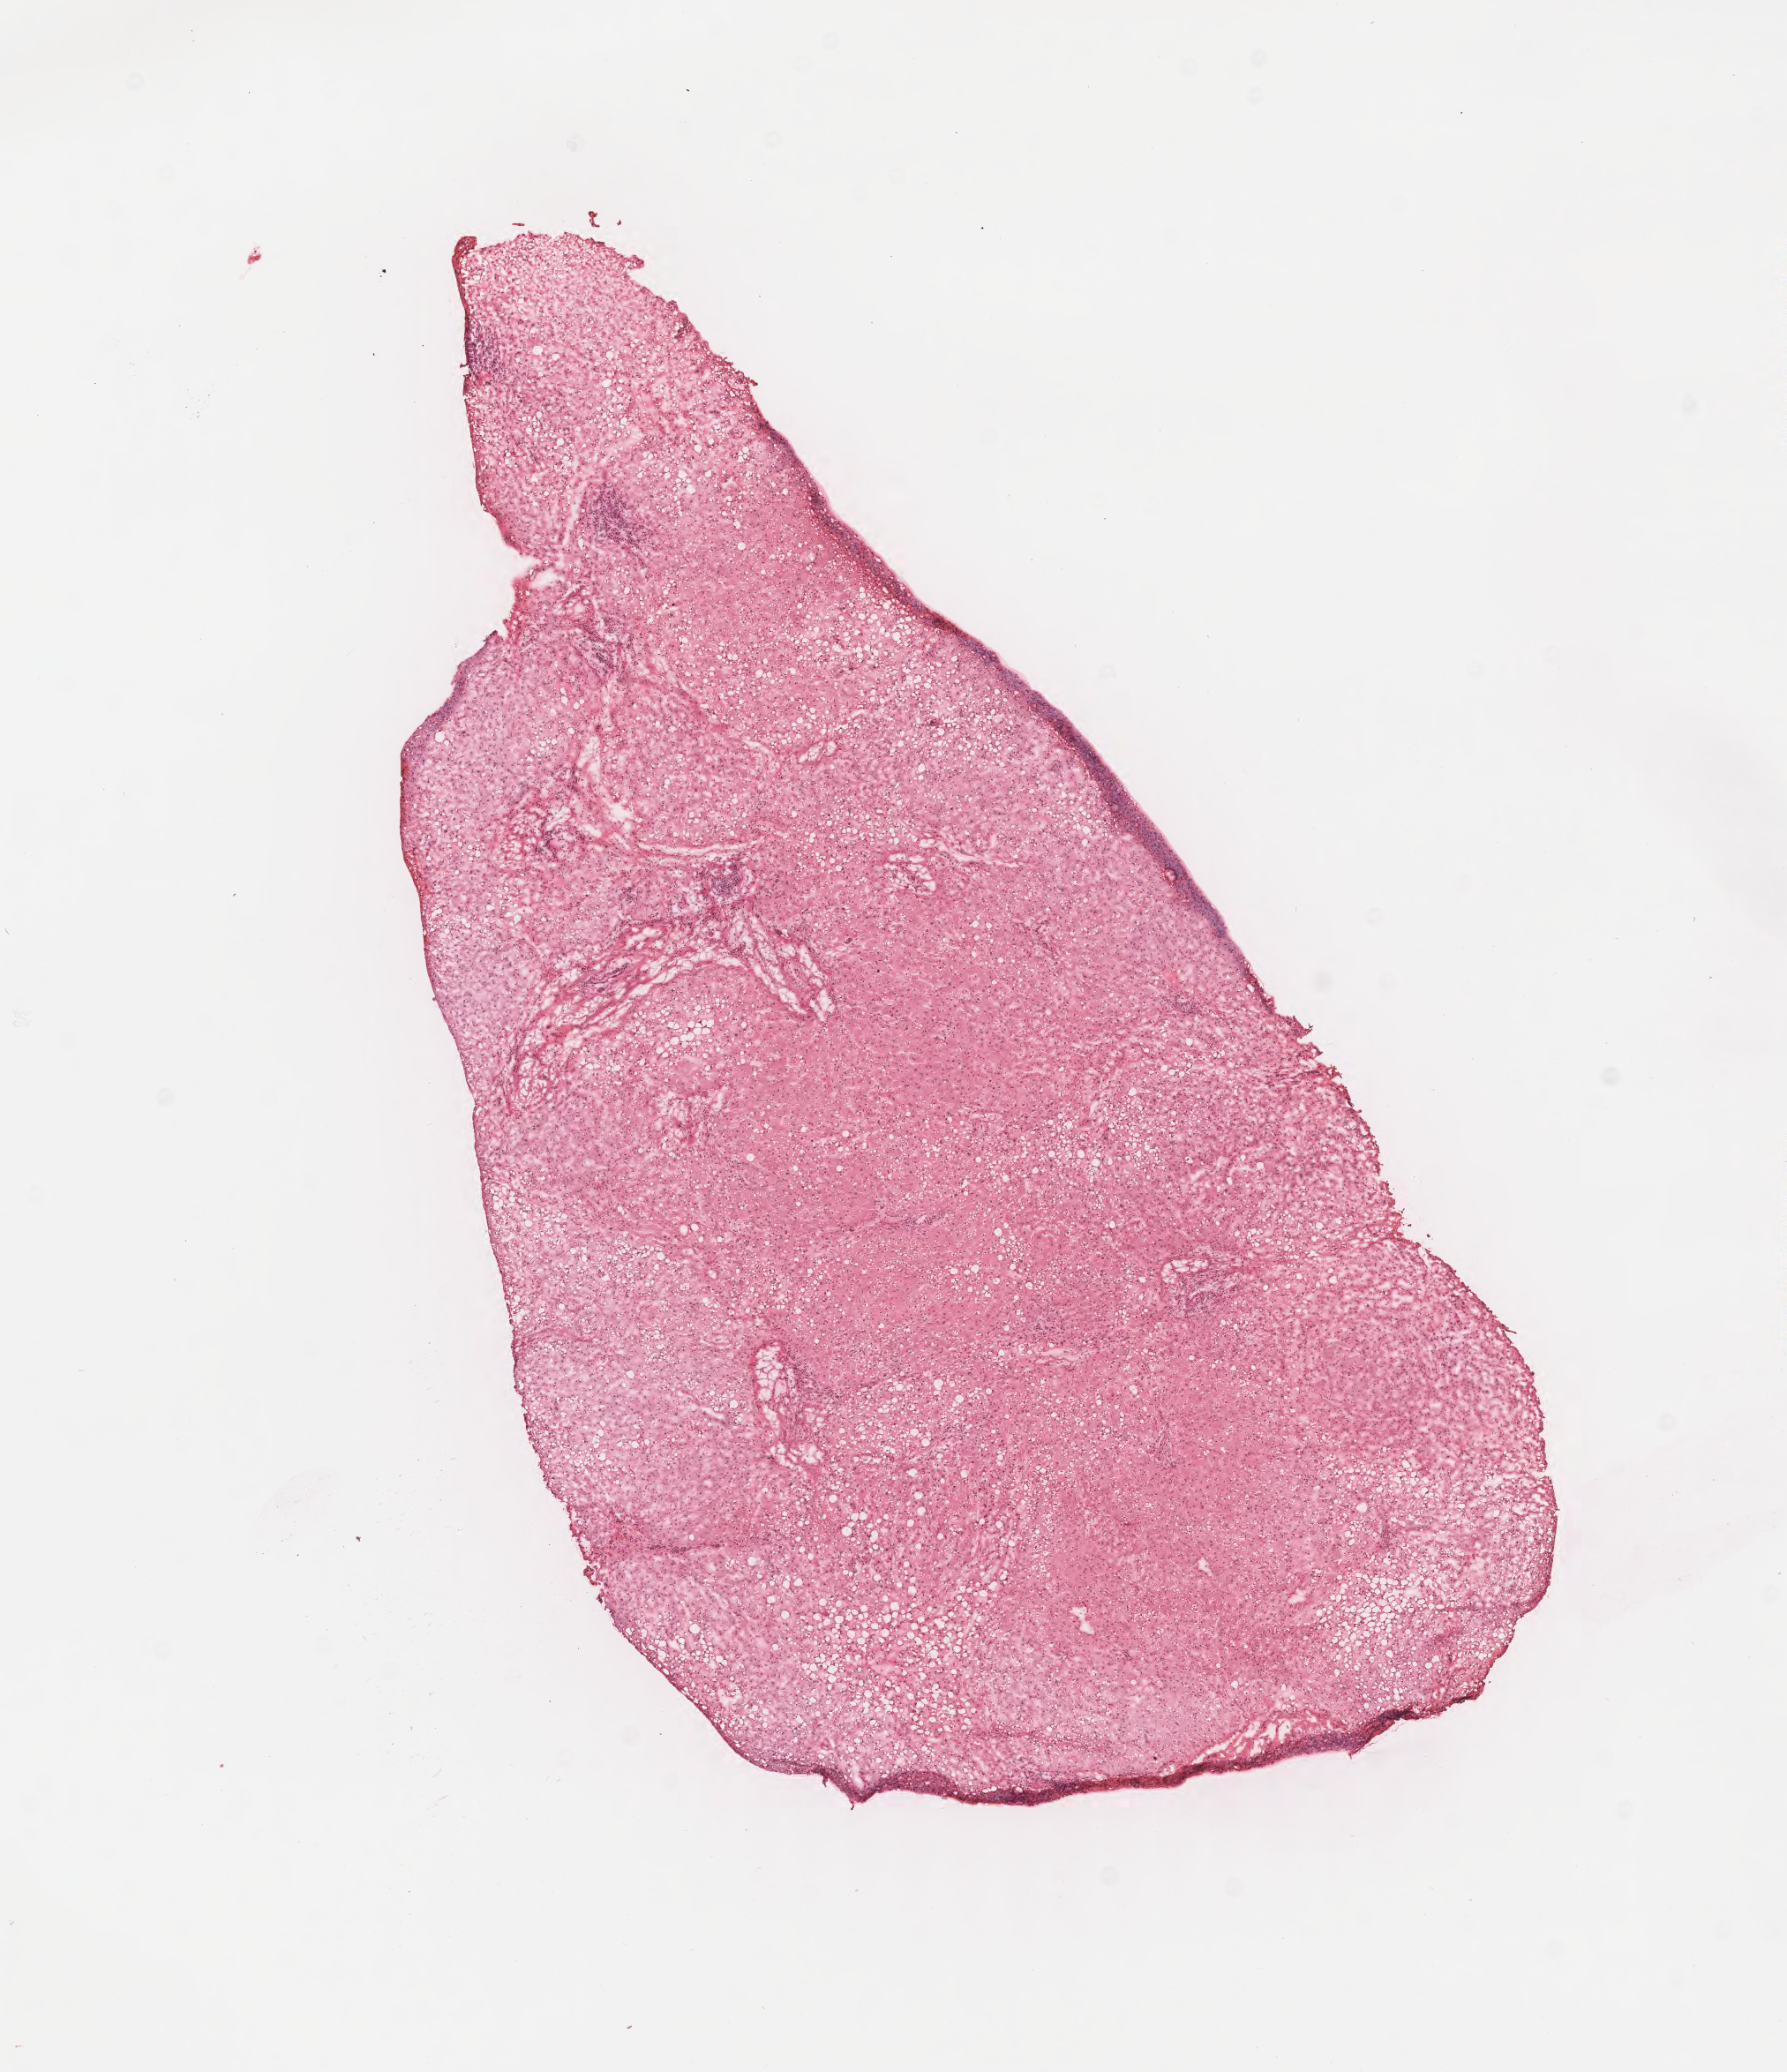
Digitized haematoxylin and eosin-stained section, shown as a low-resolution overview of the whole scanned area (about 8.0 x 9.3 mm); cryosection; specimen: non-tumor (normal tissue) sample from a patient with hepatocellular carcinoma, NOS; site: liver. Male, age 86 years at initial diagnosis. Composition of this section per pathologist review: tumor cells 0%, tumor nuclei 0%, stromal cells 10%, necrosis 0%, normal cells 90%. Infiltration values recorded for this section: lymphocyte infiltration 4%, monocyte infiltration 1%, neutrophil infiltration 2%.
This section: non-tumor tissue sample; the patient's diagnosis is given above. Section: bottom of the tissue portion.